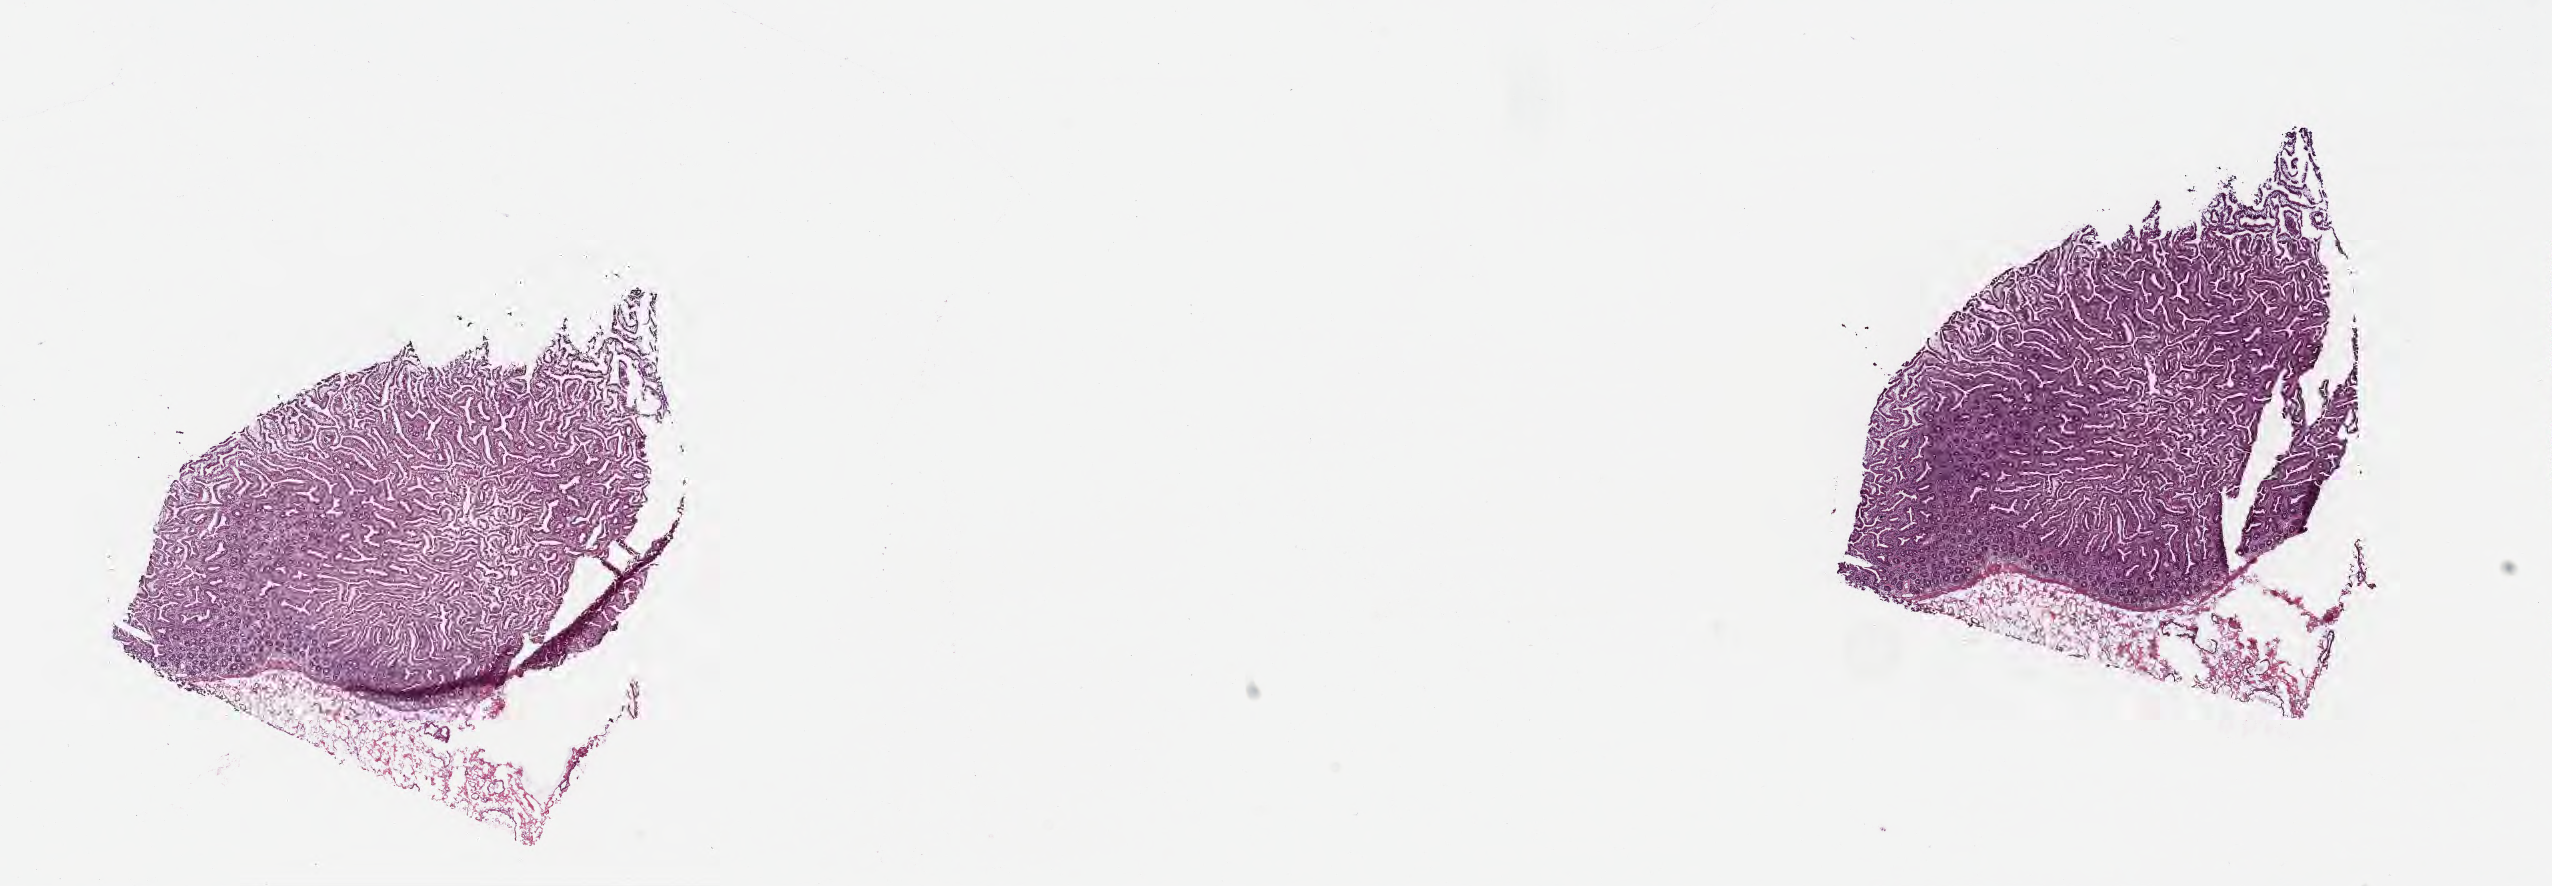
Whole-slide image, haematoxylin and eosin stain — low-resolution overview of the scanned area, about 20.6 x 7.2 mm. Frozen section (tissue freezing medium). Normal-tissue sample (non-tumor) from a patient with infiltrating duct carcinoma, NOS. Anatomic site: head of pancreas. Patient: male, age at initial diagnosis 69 years. Slide review estimates, as recorded: tumor cells 0%, tumor nuclei 0%, stromal cells 25%, necrosis 0%, normal cells 75%. Inflammatory infiltration, as recorded: lymphocyte infiltration 6%, monocyte infiltration 3%, neutrophil infiltration 5%.
This section: non-tumor tissue sample; the patient's diagnosis is given above. Section: bottom of the tissue portion.